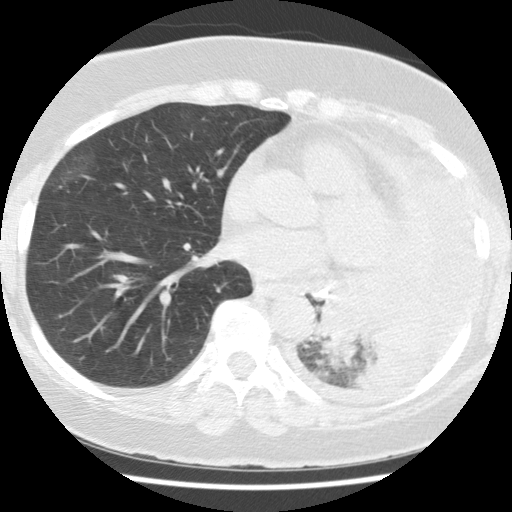
Axial slice from a low-dose chest CT screening exam, baseline annual screen, lung window (W 1500 / L -600 HU), 512 × 512 image matrix, field of view 320 × 320 mm. Female participant, aged 65 years at enrolment.
- Expert-annotated lung lesion, bounding box <310,282,426,379> (left, top, right, bottom; pixels).
- Screening reader's record for this exam (one nodule recorded; not confirmed to be the boxed lesion): non-calcified nodule or mass ≥4 mm, left lower lobe, 74 × 48 mm, spiculated (stellate) margins, soft tissue attenuation.
- Later outcome: lung cancer diagnosed 13 days after this screen — adenocarcinoma, NOS, left lower lobe, stage IV (AJCC 6th edition), 74 mm at pathology.